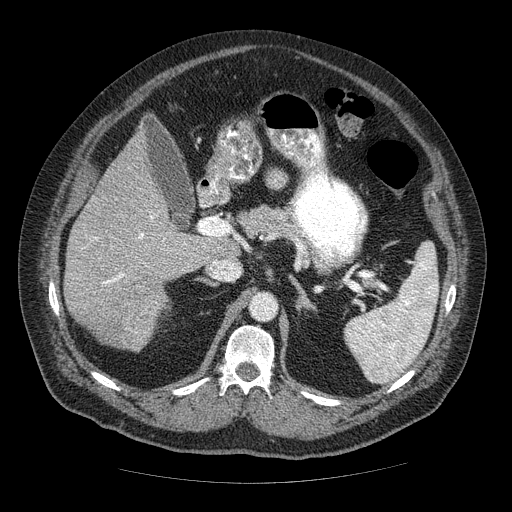
Contrast-enhanced abdominal CT (liver protocol), one axial slice. Position 30 of 85 along the scan axis. Soft-tissue window (W 400 / L 40 HU). 2.5 mm slice thickness. 512 × 512 image matrix. Case-level facts recorded for this patient, not image findings: diagnosis: hepatocellular carcinoma (patient treated with transarterial chemoembolisation; whether this scan precedes or follows treatment is not stated here); TNM stage (as recorded): Stage-IIIA; Child-Pugh class: A; tumour nodularity: multinodular.
Annotated regions visible in this slice (semi-automatically segmented with operator editing):
- liver parenchyma outside the tumour (the mass and vessels are separate outlines, so this box may not span the whole liver): box from (x=64, y=127) to (x=224, y=344) px
- mass: (x=87, y=270)–(x=167, y=351)
- liver vessels: (x=95, y=216)–(x=185, y=285)